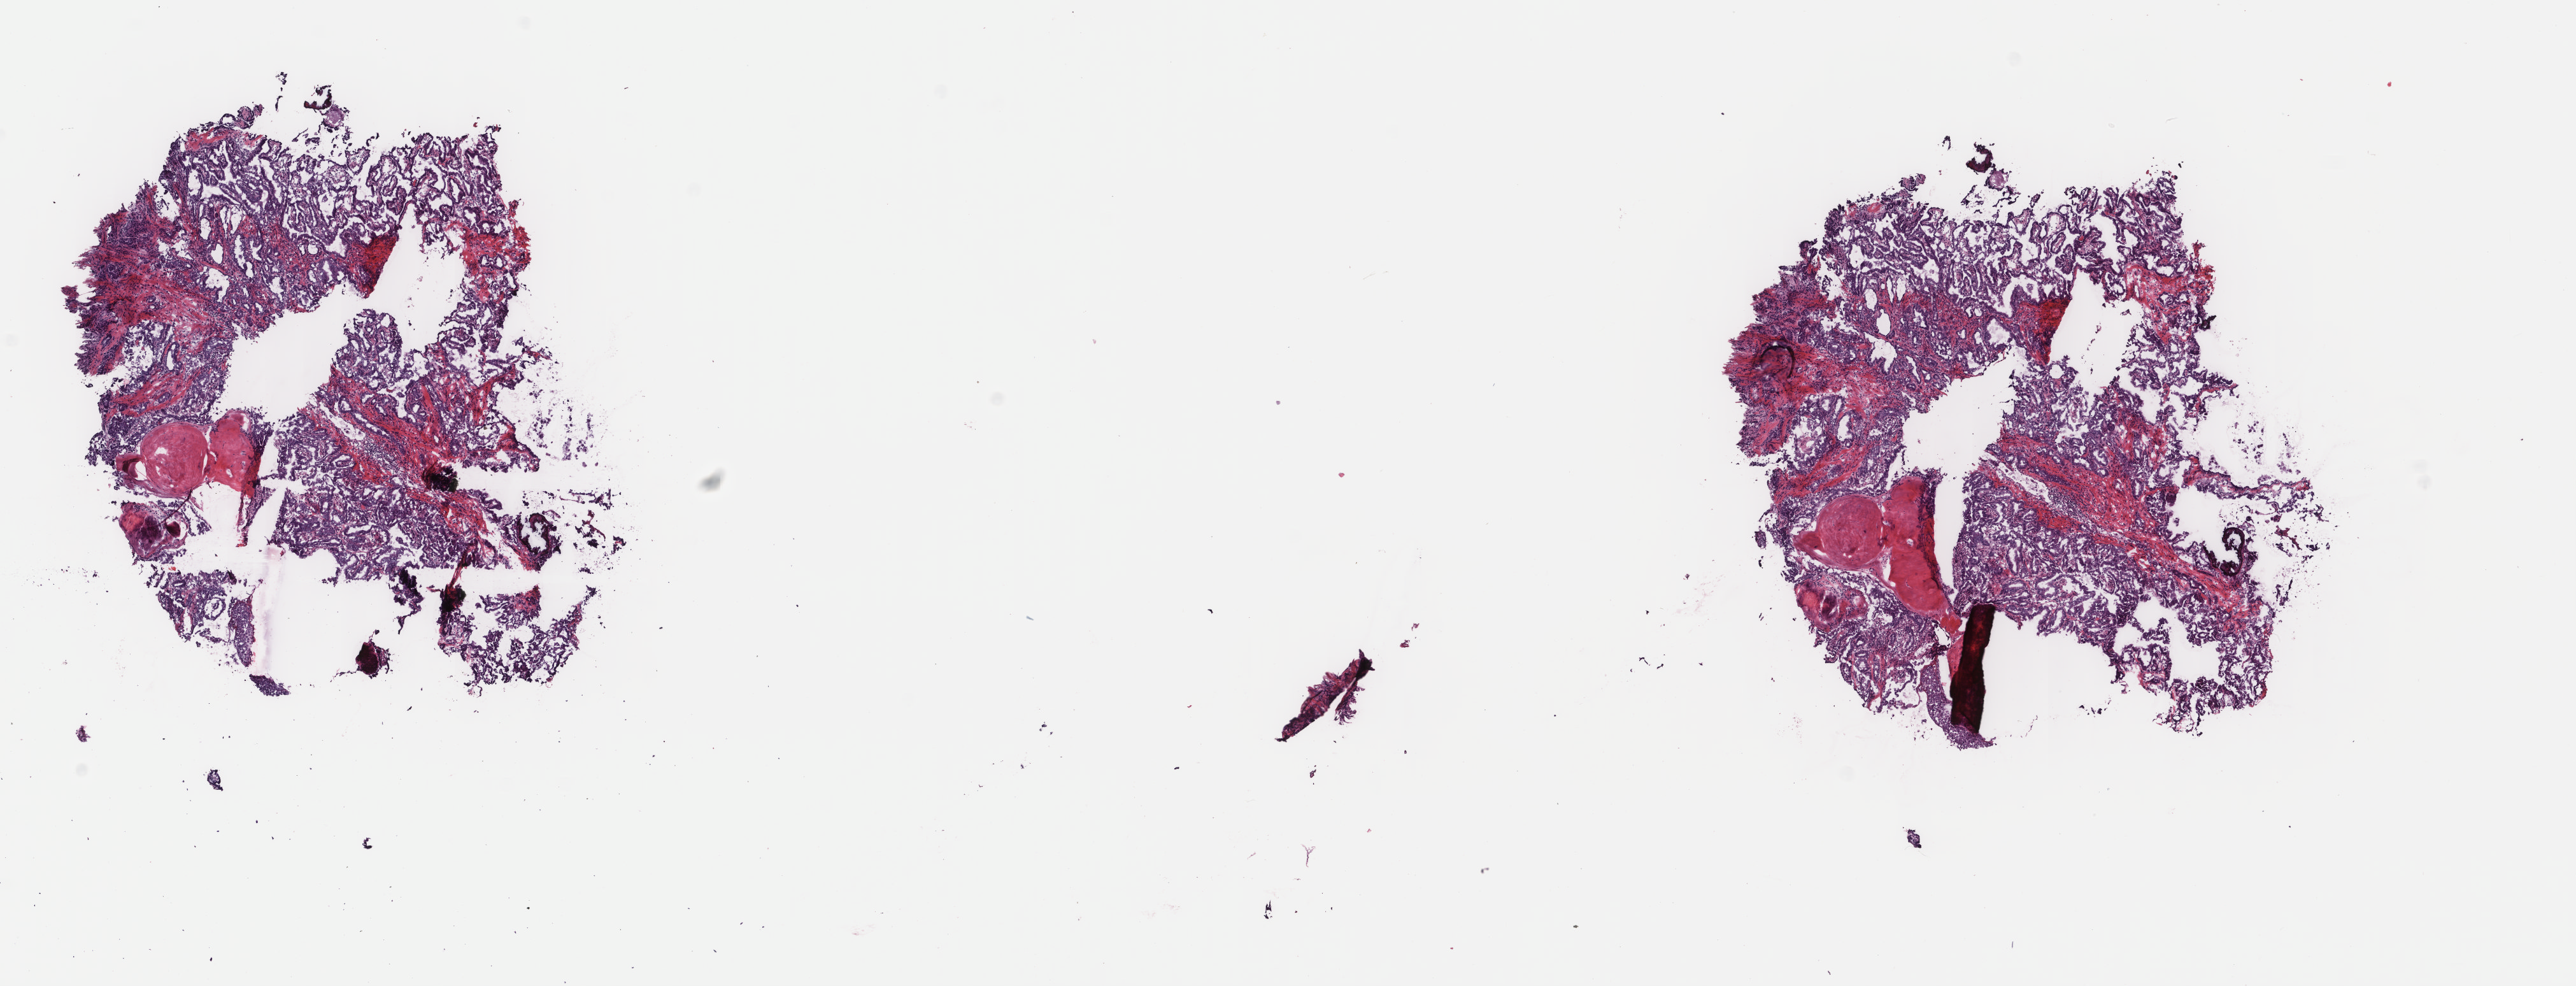
Whole-slide histology image, Hematoxylin and eosin (H&E) stained, a low-resolution overview of the entire scanned area, about 16.1 x 6.1 mm. Frozen section from the top of the tissue portion. Thyroid, primary tumour sample. Patient: male, age at initial diagnosis 34 years. Composition of this section per pathologist review: tumour cells 100%, tumour nuclei 93%, normal cells 0%, stromal cells 0%, necrosis 0%. Infiltration values recorded for this section: lymphocyte infiltration 0%, monocyte infiltration 0%, neutrophil infiltration 0%.
TNM: T2 NX MX. Pathologic diagnosis: Papillary adenocarcinoma, NOS (thyroid gland). AJCC pathologic stage: I (6th edition).